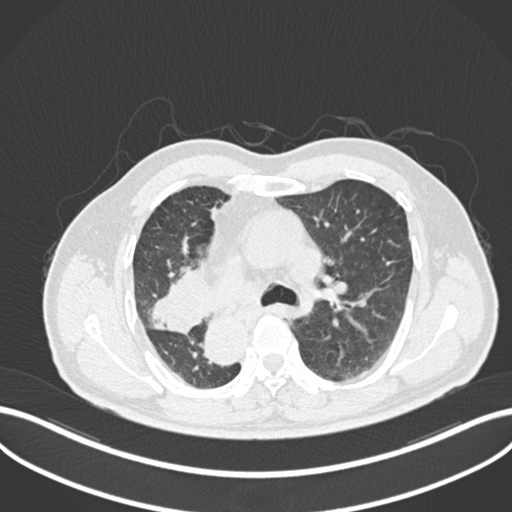
Chest CT, one axial slice. Slice 154 of 206 in the series (ordered by position). Reconstruction kernel B30f. Lung window (W 1500 / L -600 HU). 512 × 512 image matrix. Patient: male, 67 years. From the clinical record (not read from this slice): clinical TNM (as recorded): T2a N0 M0.
Annotated regions visible in this slice (bounding box drawn by a radiologist):
- lung tumour (recorded histology: squamous cell carcinoma): box from (x=144, y=273) to (x=213, y=336) px